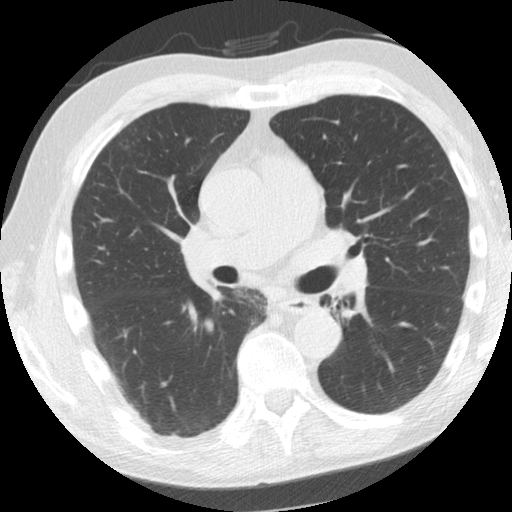
Chest CT (low-dose screening protocol), one axial image; second annual screen; lung window (W 1500 / L -600 HU); 2.5 mm slice thickness; slice 70 of 156 in the series. Male participant, aged 61 years at enrolment. Former smoker at enrolment.
Lesion marked by an expert reader, bounding box <303,288,348,324> (left, top, right, bottom; pixels). No non-calcified nodule or mass ≥4 mm was recorded by the screening reader at this exam. Later outcome: lung cancer diagnosed 775 days after this screen (after the third annual screen) — squamous cell carcinoma, NOS, left upper lobe, left lower lobe, well differentiated (G1), stage IIB (AJCC 6th edition), 100 mm at pathology.